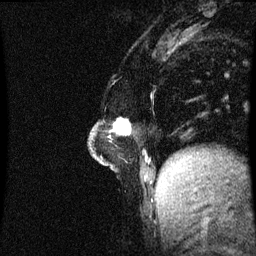
Breast MRI (dynamic contrast-enhanced), one sagittal slice. Position 16 of 60 along the scan axis. Dynamic contrast-enhanced series, image 2 of 3 at this slice position (ordered by acquisition). 1.5 T. TE 4.2 ms, TR 8.9 ms. 256 × 256 image matrix, field of view 200 × 200 mm. Patient: female, 47 years. From the clinical record (not read from this slice): setting: breast cancer imaged before/during neoadjuvant chemotherapy; receptor status: HR-positive, HER2-negative.
Annotated regions visible in this slice (semi-automatically segmented with operator editing):
- analysis volume of interest (the breast-tissue region the enhancement analysis was run in; not a lesion): bounding box [x1, y1, x2, y2] px = [92, 122, 129, 163]
- tumour enhancement mask (voxels above the 70 % enhancement threshold inside the analysis volume of interest): [116, 122, 129, 135]